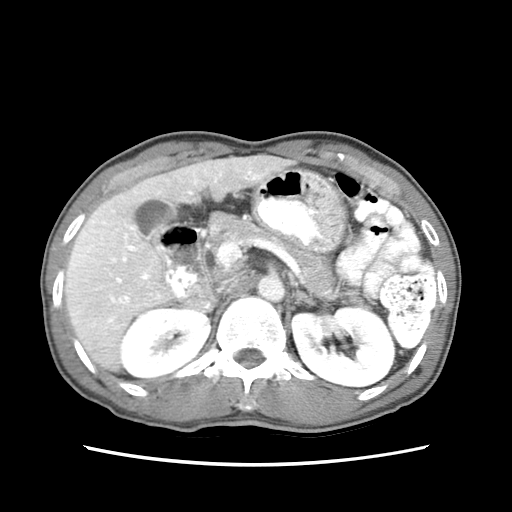
Contrast-enhanced abdominal CT (liver protocol), one axial slice; position 35 of 79 along the scan axis; 120 kVp; soft-tissue window (W 400 / L 40 HU); 2.5 mm slice thickness; 512 × 512 image matrix. Case-level facts recorded for this patient, not image findings: diagnosis: hepatocellular carcinoma (patient treated with transarterial chemoembolisation; whether this scan precedes or follows treatment is not stated here); TNM stage (as recorded): Stage-IIIB; Child-Pugh class: A.
Annotated regions visible in this slice (semi-automatically segmented with operator editing):
- liver parenchyma outside the tumour (the mass and vessels are separate outlines, so this box may not span the whole liver): bounding box [x1, y1, x2, y2] px = [66, 152, 294, 370]
- mass: [70, 253, 102, 267]
- liver vessels: [74, 162, 277, 328]